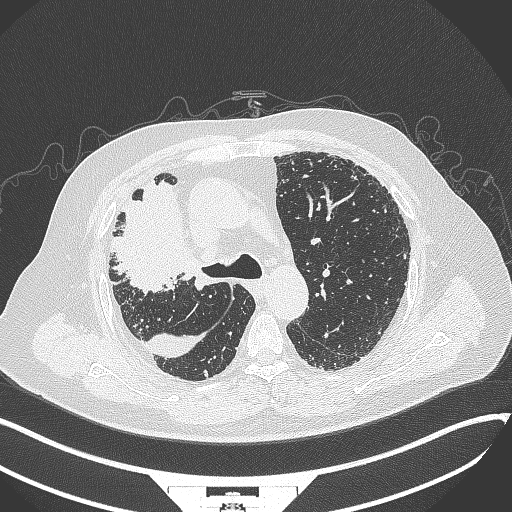
Chest CT, one axial slice. Position 239 of 384 along the scan axis. Reconstruction kernel B70f. 120 kVp. Lung window (W 1500 / L -600 HU). 512 × 512 image matrix, field of view 400 × 400 mm. Patient: male, 69 years. From the clinical record (not read from this slice): clinical TNM (as recorded): T4 N3 M1.
Annotated regions visible in this slice (rectangle marked by the reading radiologist):
- lung tumour (recorded histology: adenocarcinoma): bounding box (x1, y1, x2, y2) in pixels: (105, 185, 194, 296)